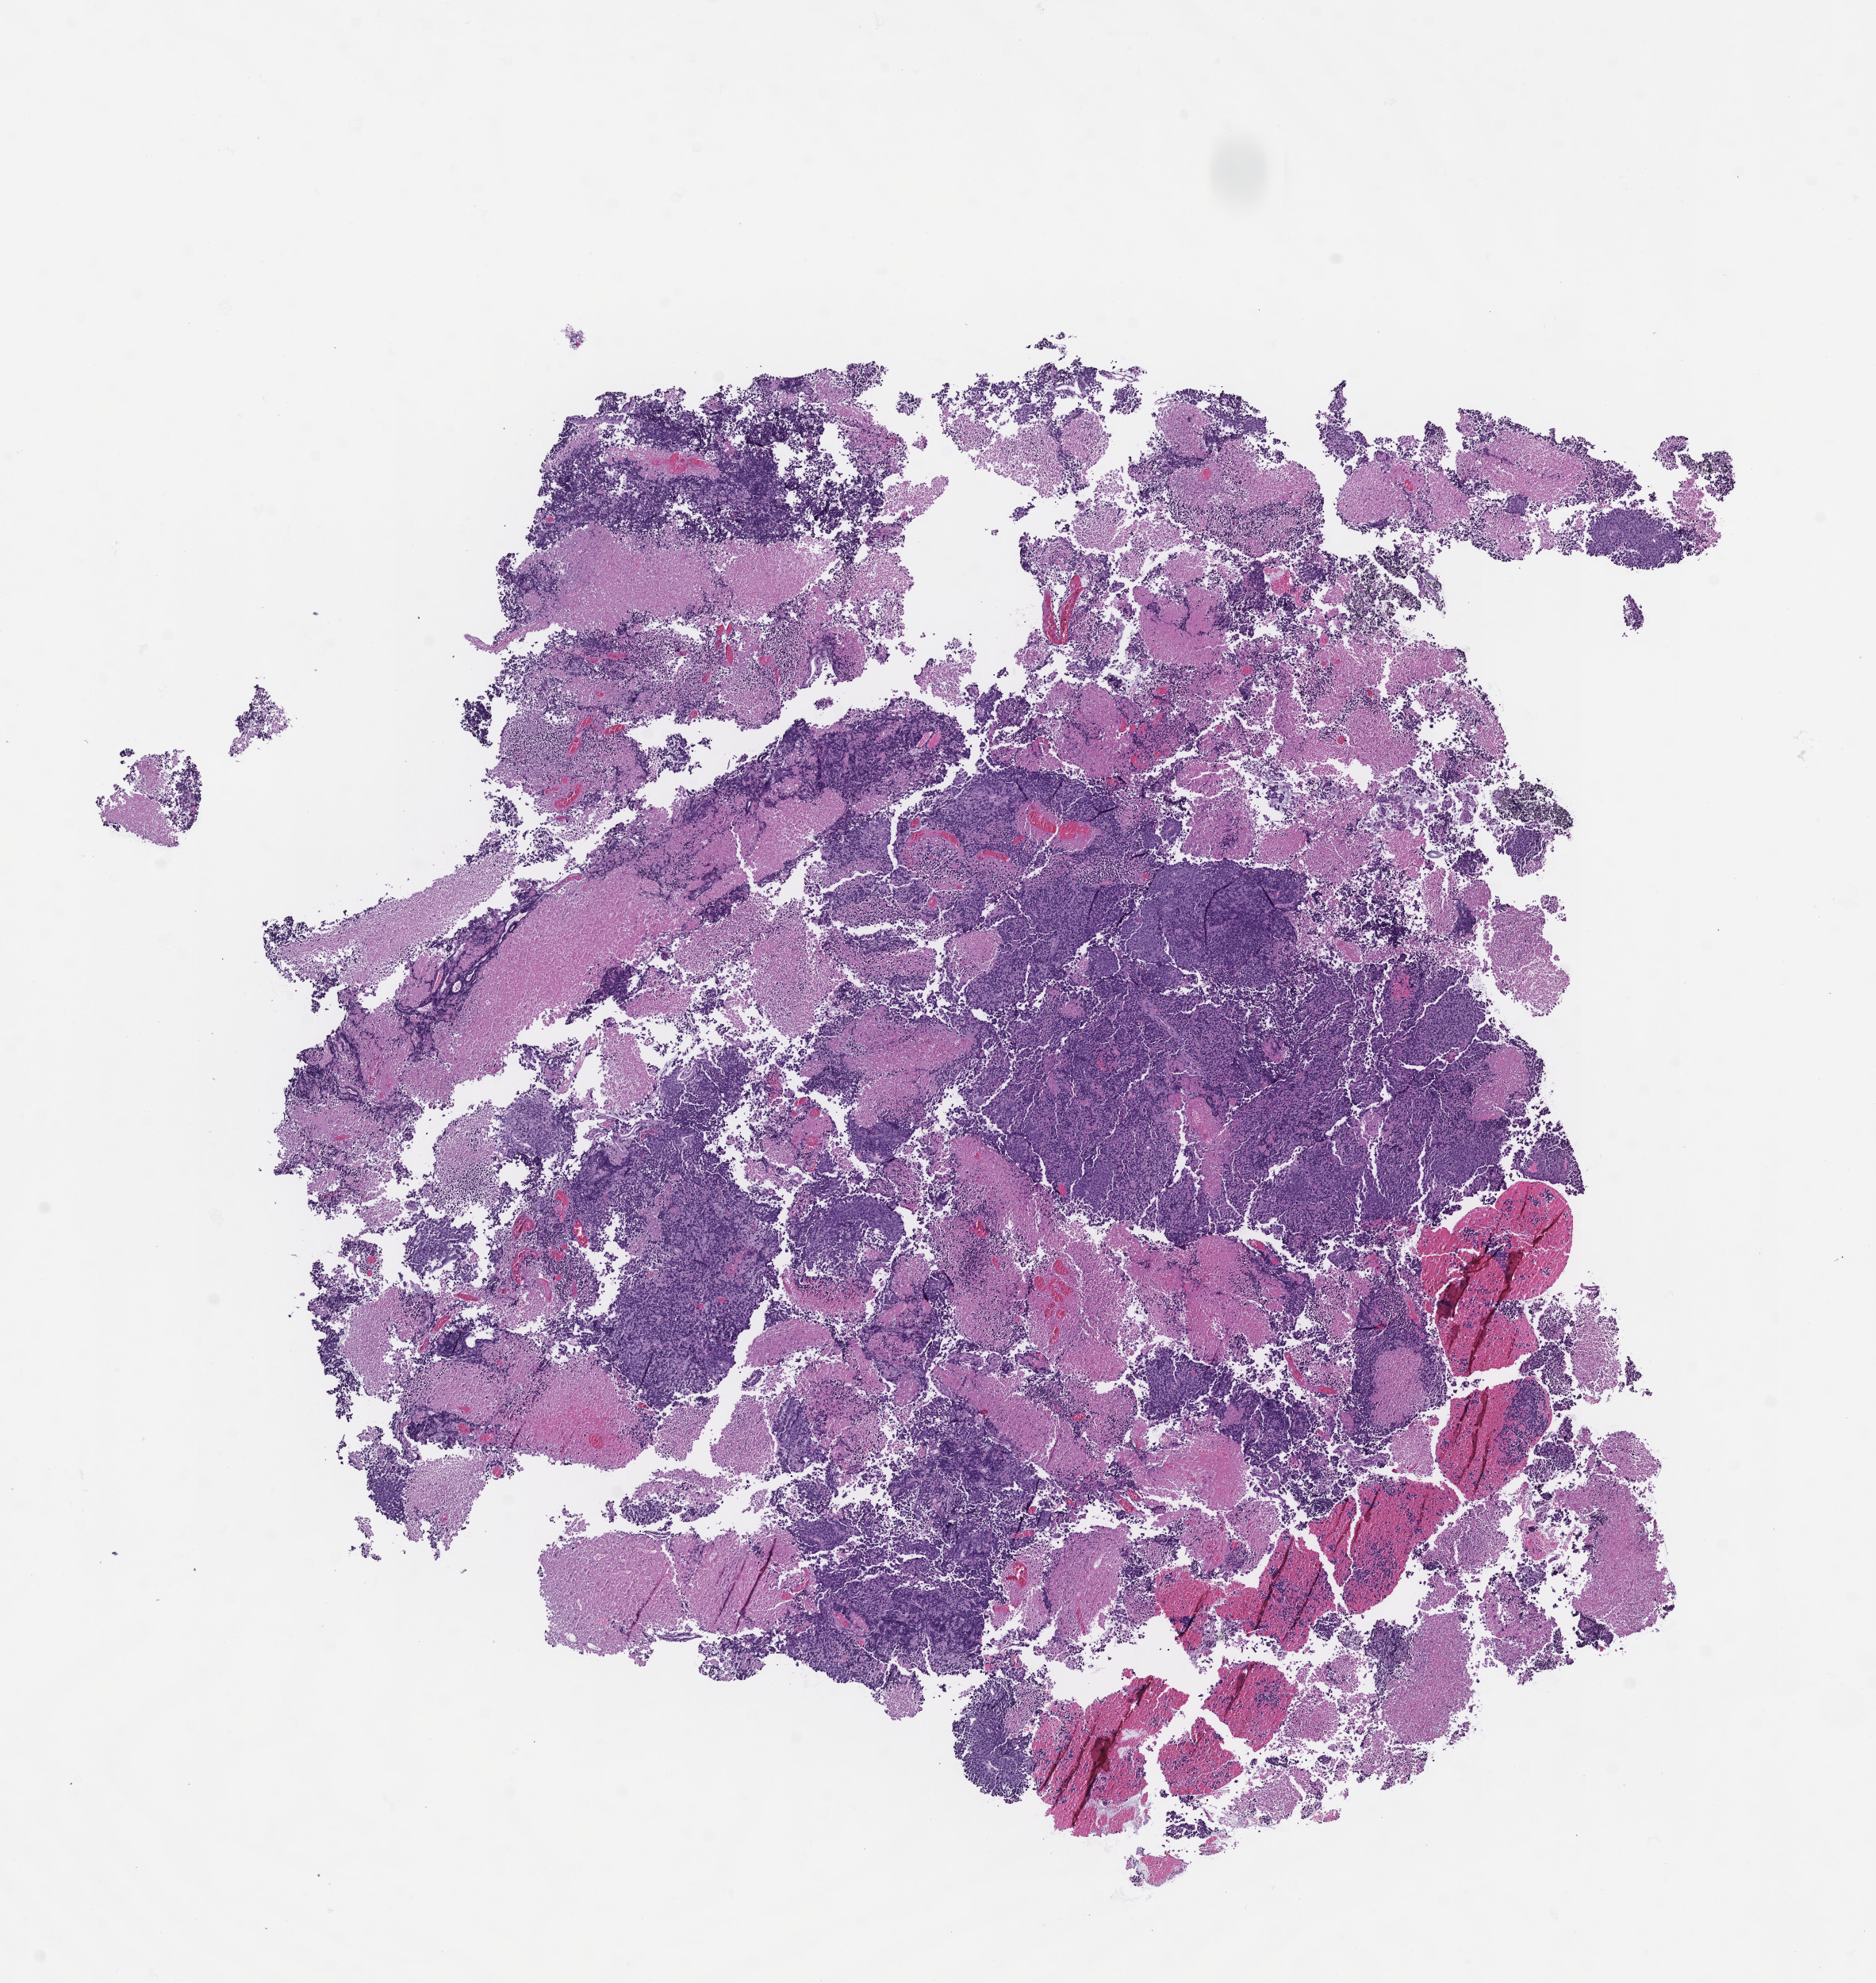
H&E whole-slide image, low-resolution overview of the scanned area, about 9.5 x 10.1 mm. Formalin-fixed, paraffin-embedded (FFPE) tissue. Patient: male.
This section: metastasis (sampled organ not recorded). Primary diagnosis of the patient: Small Cell Lung Carcinoma.